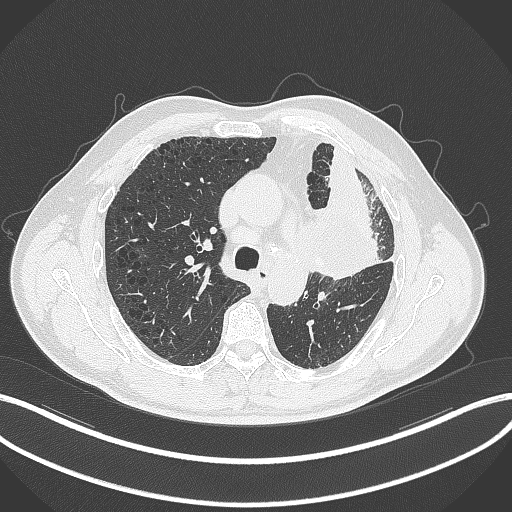
Chest CT, one axial slice. Slice 208 of 297 in the series (ordered by position). Reconstruction kernel B70f. 120 kVp. Lung window (W 1500 / L -600 HU). 1 mm slice thickness. 512 × 512 image matrix, field of view 400 × 400 mm. Male patient, age 68 years. Case-level facts recorded for this patient, not image findings: clinical TNM (as recorded): T3 N3 M1.
Annotated regions visible in this slice (bounding box drawn by a radiologist):
- lung tumour (recorded histology: adenocarcinoma): box from (x=309, y=194) to (x=386, y=281) px